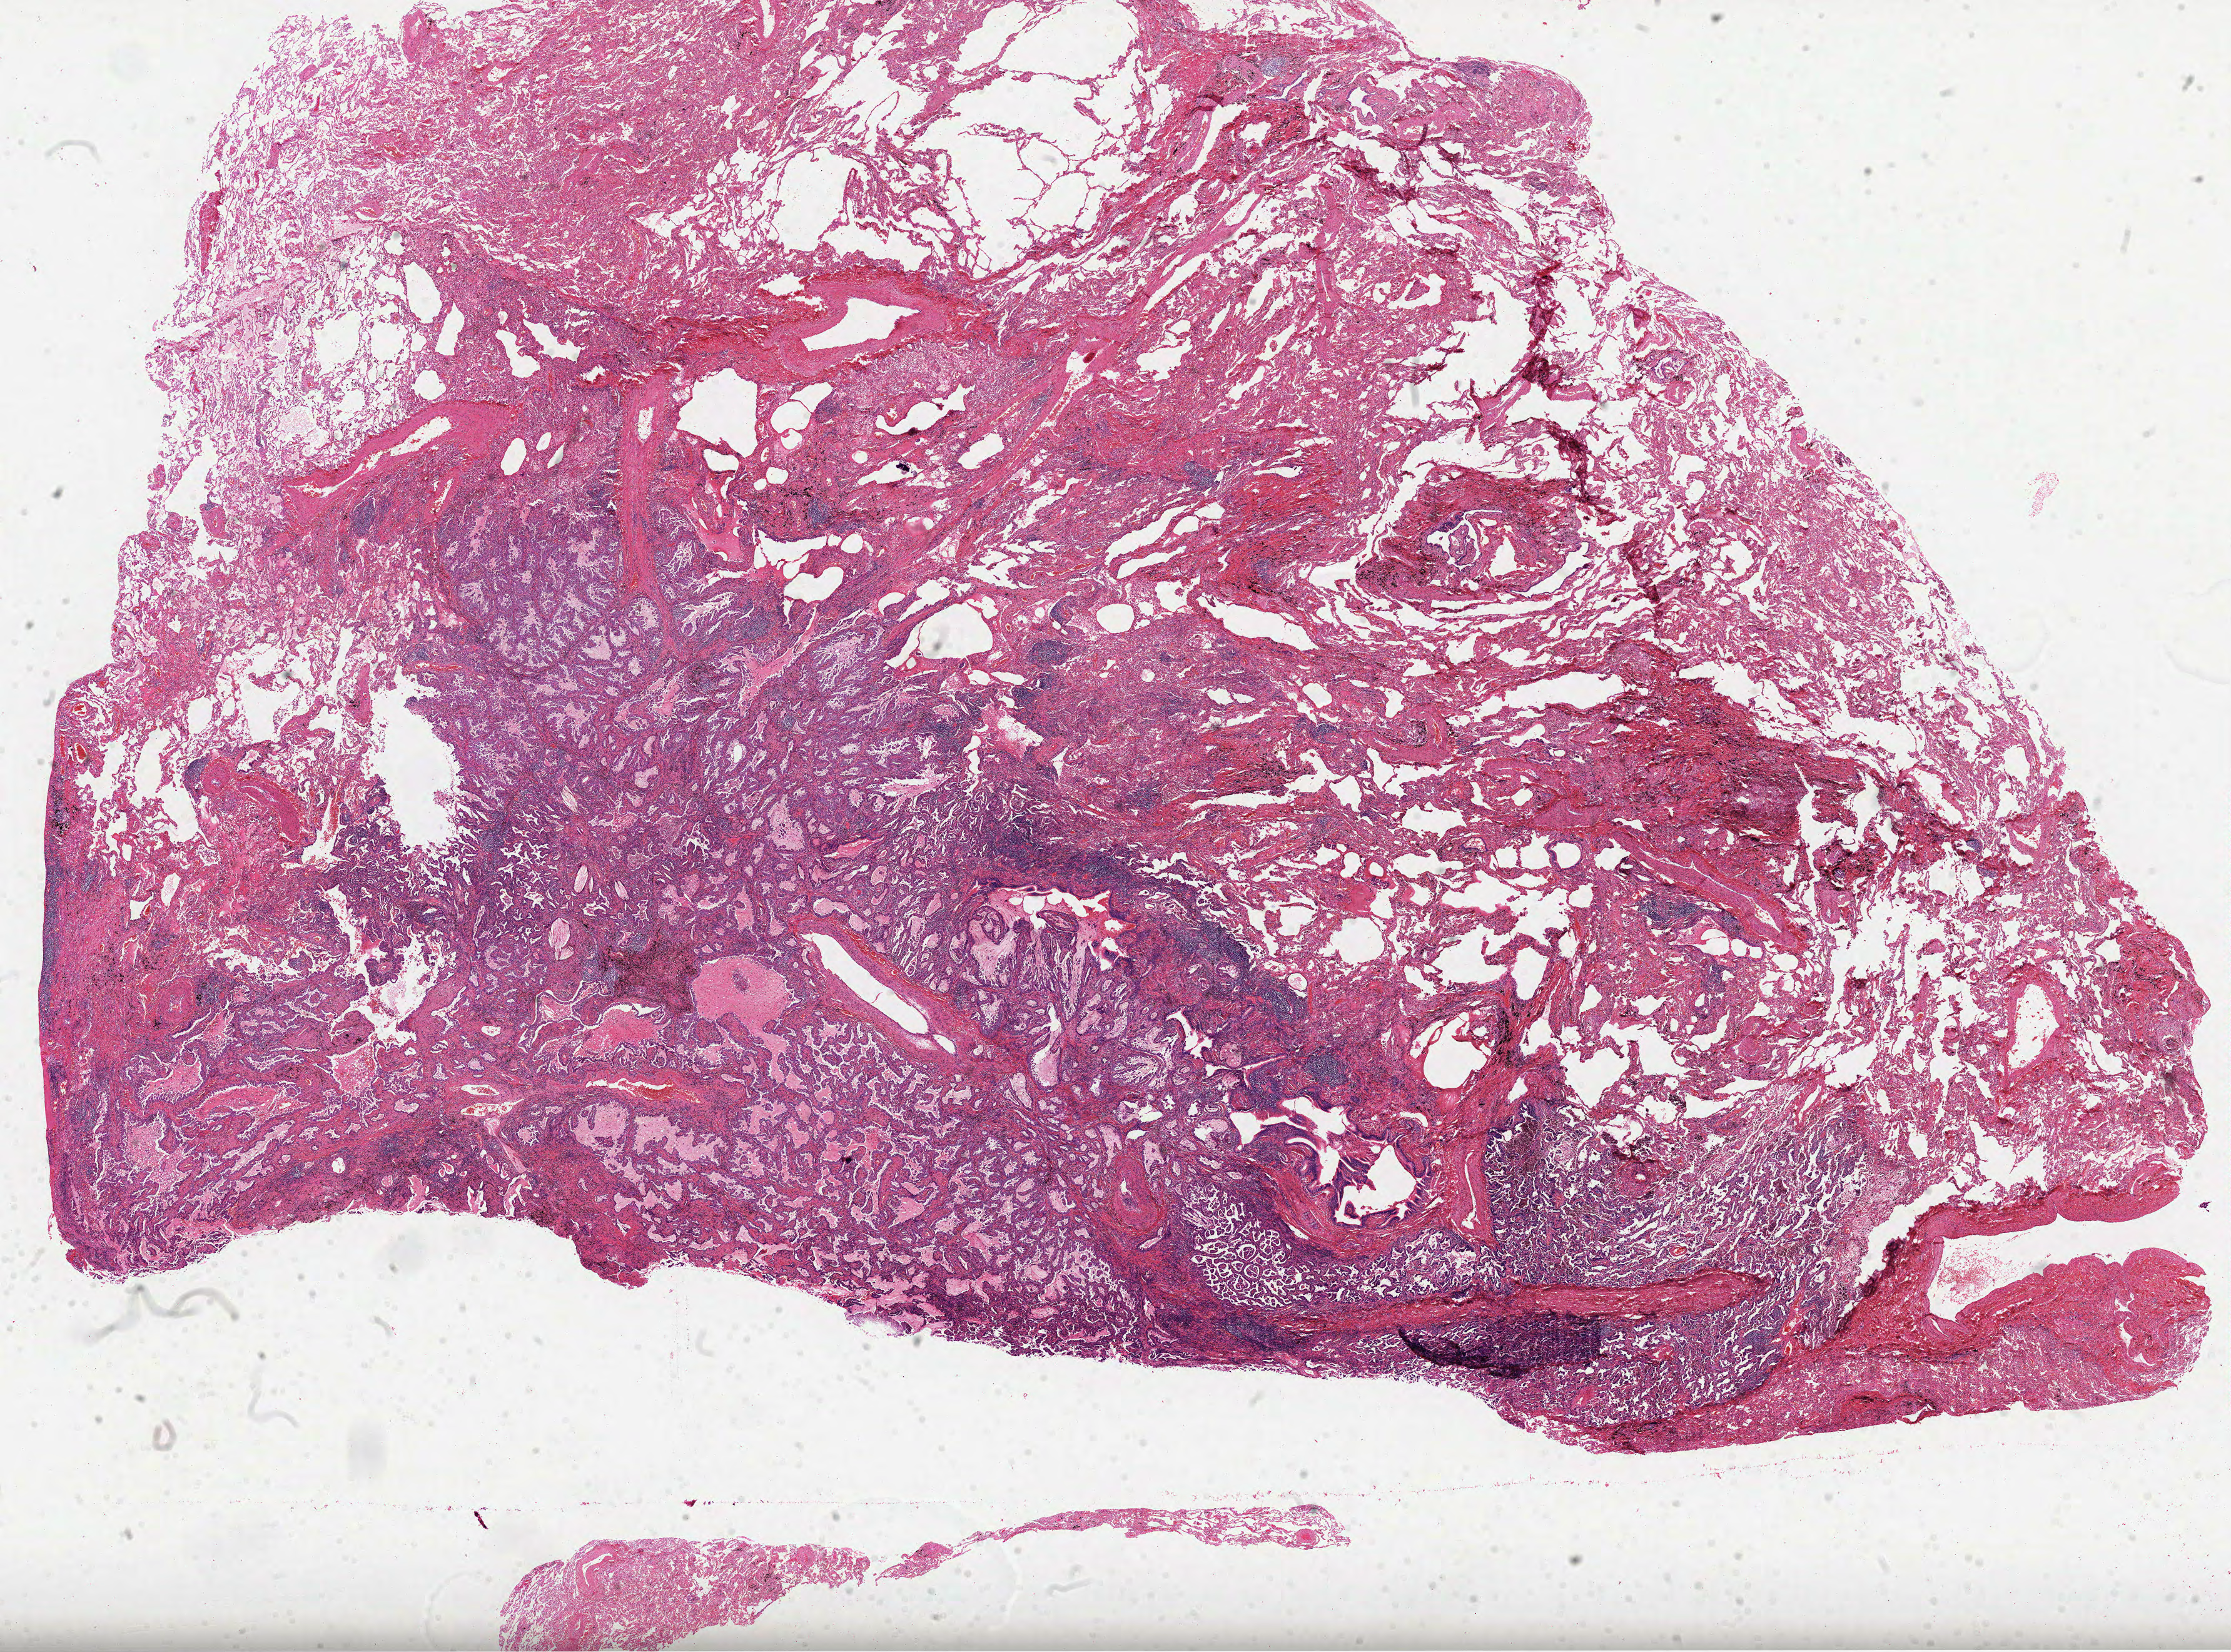
Whole-slide histology image, H&E-stained — whole scanned area (about 28.8 x 21.3 mm) shown as a low-resolution overview. Formalin-fixed paraffin-embedded (FFPE) diagnostic section. Lung, primary tumour sample. Patient: male, age at initial diagnosis 65 years.
* laterality: right
* pathologic diagnosis: Adenocarcinoma with mixed subtypes (upper lobe, lung)
* AJCC pathologic stage: IB (6th edition)